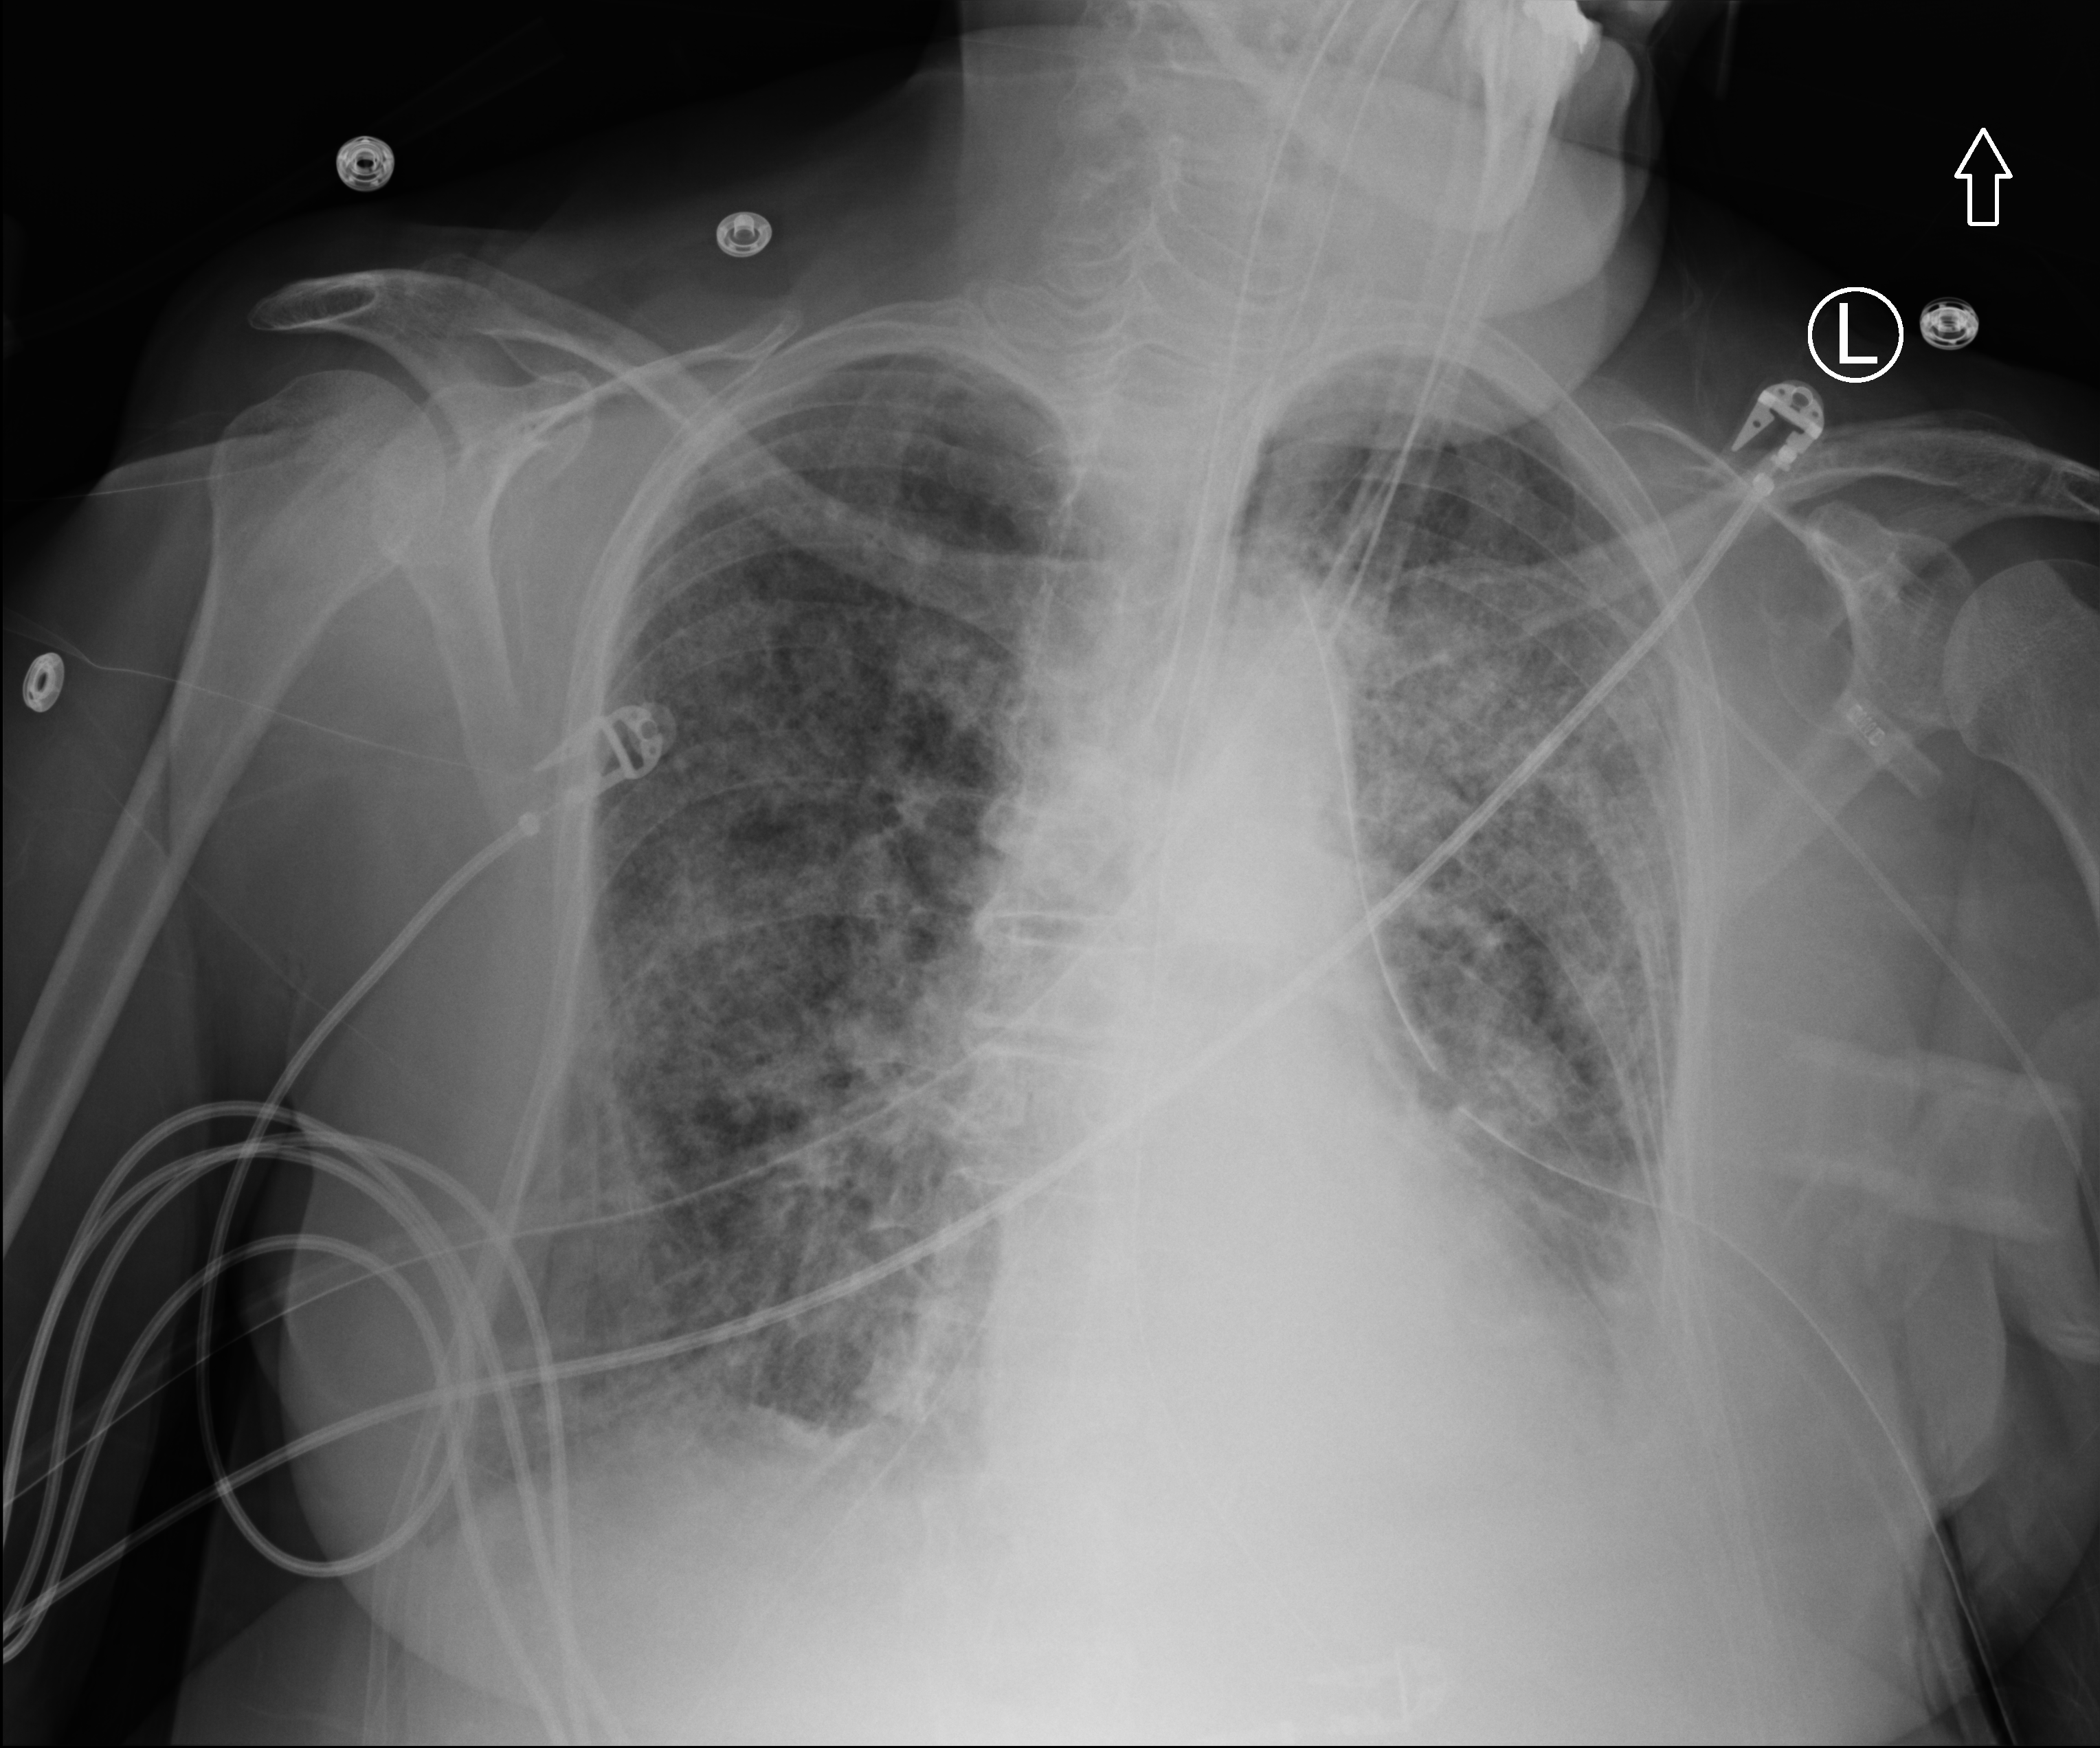
Portable chest radiograph; anteroposterior (AP) projection. Female patient hospitalised with COVID-19, age 75–90 years.
From the hospital-stay record, not from the radiograph (when in the stay this image was taken is not recorded): admitted to intensive care during this hospital stay: yes; mechanically ventilated during this hospital stay: yes; other chronic lung disease (admission record): yes.